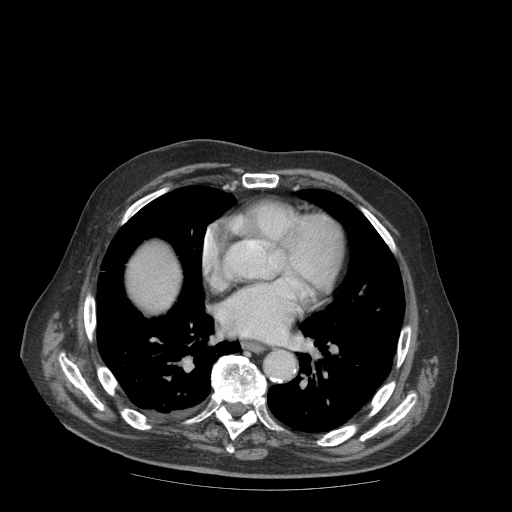
Contrast-enhanced abdominal CT (liver protocol), one axial slice; position 96 of 99 along the scan axis; reconstruction kernel STANDARD; soft-tissue window (W 400 / L 40 HU); 2.5 mm slice thickness; 512 × 512 image matrix. Case-level facts recorded for this patient, not image findings: diagnosis: hepatocellular carcinoma (patient treated with transarterial chemoembolisation; whether this scan precedes or follows treatment is not stated here); TNM stage (as recorded): Stage-IIIB; Child-Pugh class: A; tumour differentiation: well differentiated.
Structures marked on this image (semi-automatic segmentation, software-assisted and operator-edited):
- liver parenchyma outside the tumour (the mass and vessels are separate outlines, so this box may not span the whole liver): bounding box <128,242,180,312> (left, top, right, bottom; pixels)